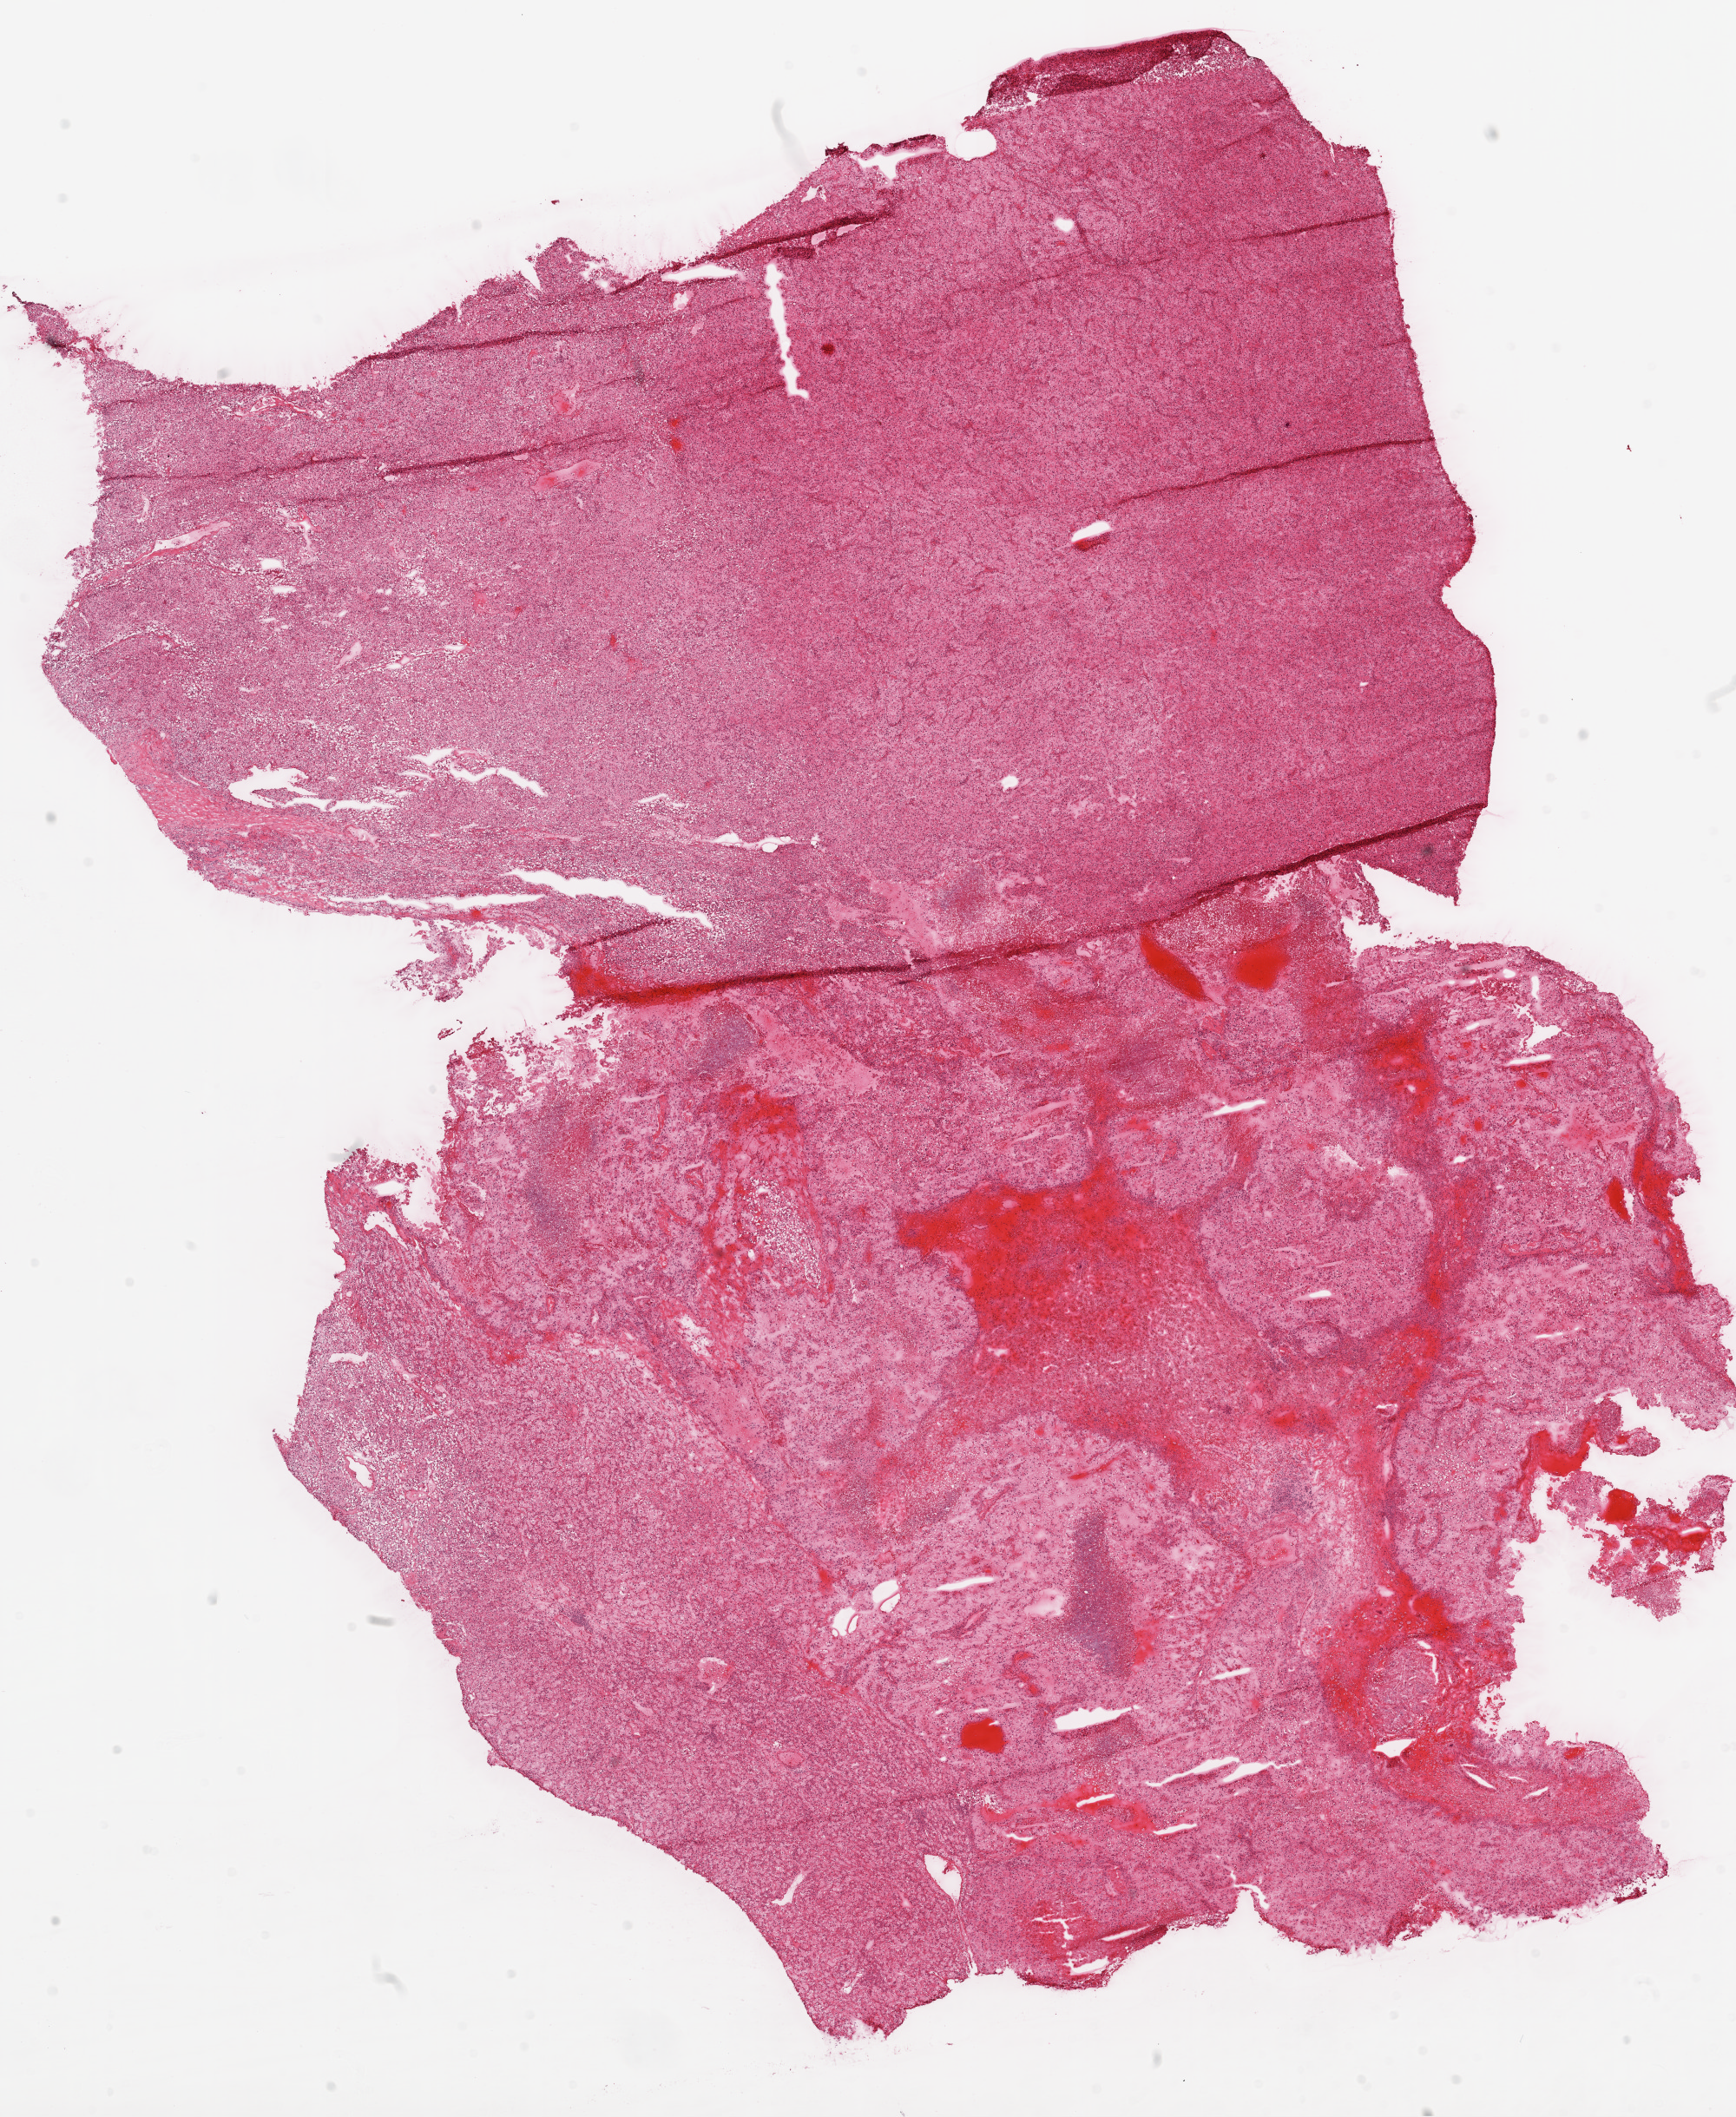
Digitized H&E tissue section (whole slide) — low-resolution overview of the scanned area, about 16.0 x 19.6 mm (acquisition: 20x scan); frozen section from the top of the tissue portion; sample: primary tumour, kidney. Male patient; age at initial diagnosis 74 years. Histologic grade: G3 (poorly differentiated). Composition of this section per pathologist review: tumour cells 95%, tumour nuclei 85%, normal cells 0%, stromal cells 5%, necrosis 0%.
* AJCC pathologic stage: I
* histologic diagnosis: Clear cell adenocarcinoma, NOS
* TNM: T1b NX M0